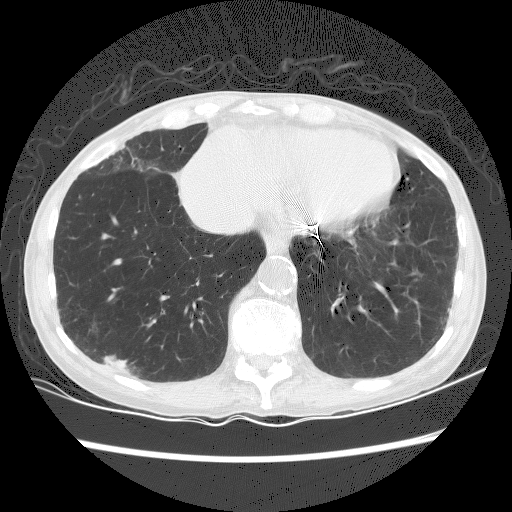
Axial slice from a low-dose chest CT screening exam. Baseline screening round. Lung window (W 1500 / L -600 HU). 2.5 mm slice thickness. Slice 100 of 156 in the series. Female participant, aged 70 years at enrolment. Current smoker at enrolment.
Expert reader's lesion annotation, bounding box (x1, y1, x2, y2) in pixels: (95, 344, 147, 385). The screening reader recorded 2 non-calcified nodules or masses ≥4 mm on this exam (right lower lobe, left lower lobe); which of them this box marks is not recorded. Official screen result: positive, change unspecified: nodule(s) >= 4 mm or enlarging nodule(s), mass(es), or other non-specific abnormalities suspicious for lung cancer. Lung cancer was diagnosed 125 days after this screen: squamous cell carcinoma, NOS, right lower lobe, well differentiated (G1), stage IA (AJCC 6th edition), 25 mm at pathology.